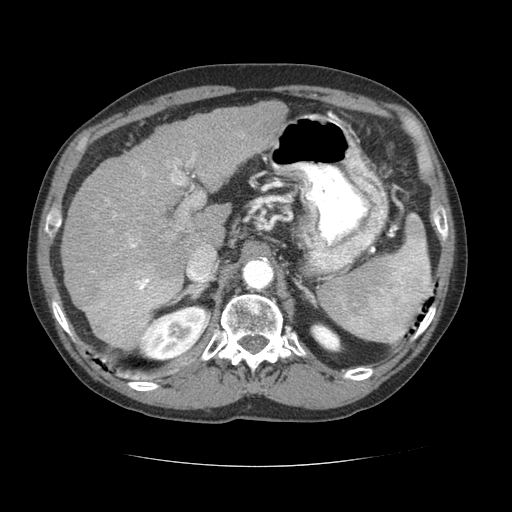
Contrast-enhanced abdominal CT (liver protocol), one axial slice; slice 47 of 69 in the series (ordered by position); reconstruction kernel STANDARD; soft-tissue window (W 400 / L 40 HU); 2.5 mm slice thickness; 512 × 512 image matrix, field of view 360 × 360 mm. Case-level facts recorded for this patient, not image findings: diagnosis: hepatocellular carcinoma (patient treated with transarterial chemoembolisation; whether this scan precedes or follows treatment is not stated here); TNM stage (as recorded): Stage-II; Child-Pugh class: B; tumour differentiation: poorly differentiated; tumour nodularity: multinodular.
Structures marked on this image (semi-automatic segmentation, software-assisted and operator-edited):
- liver parenchyma outside the tumour (the mass and vessels are separate outlines, so this box may not span the whole liver): bounding box (x1, y1, x2, y2) in pixels: (60, 100, 288, 336)
- mass: (83, 264, 180, 350)
- liver vessels: (106, 152, 204, 304)